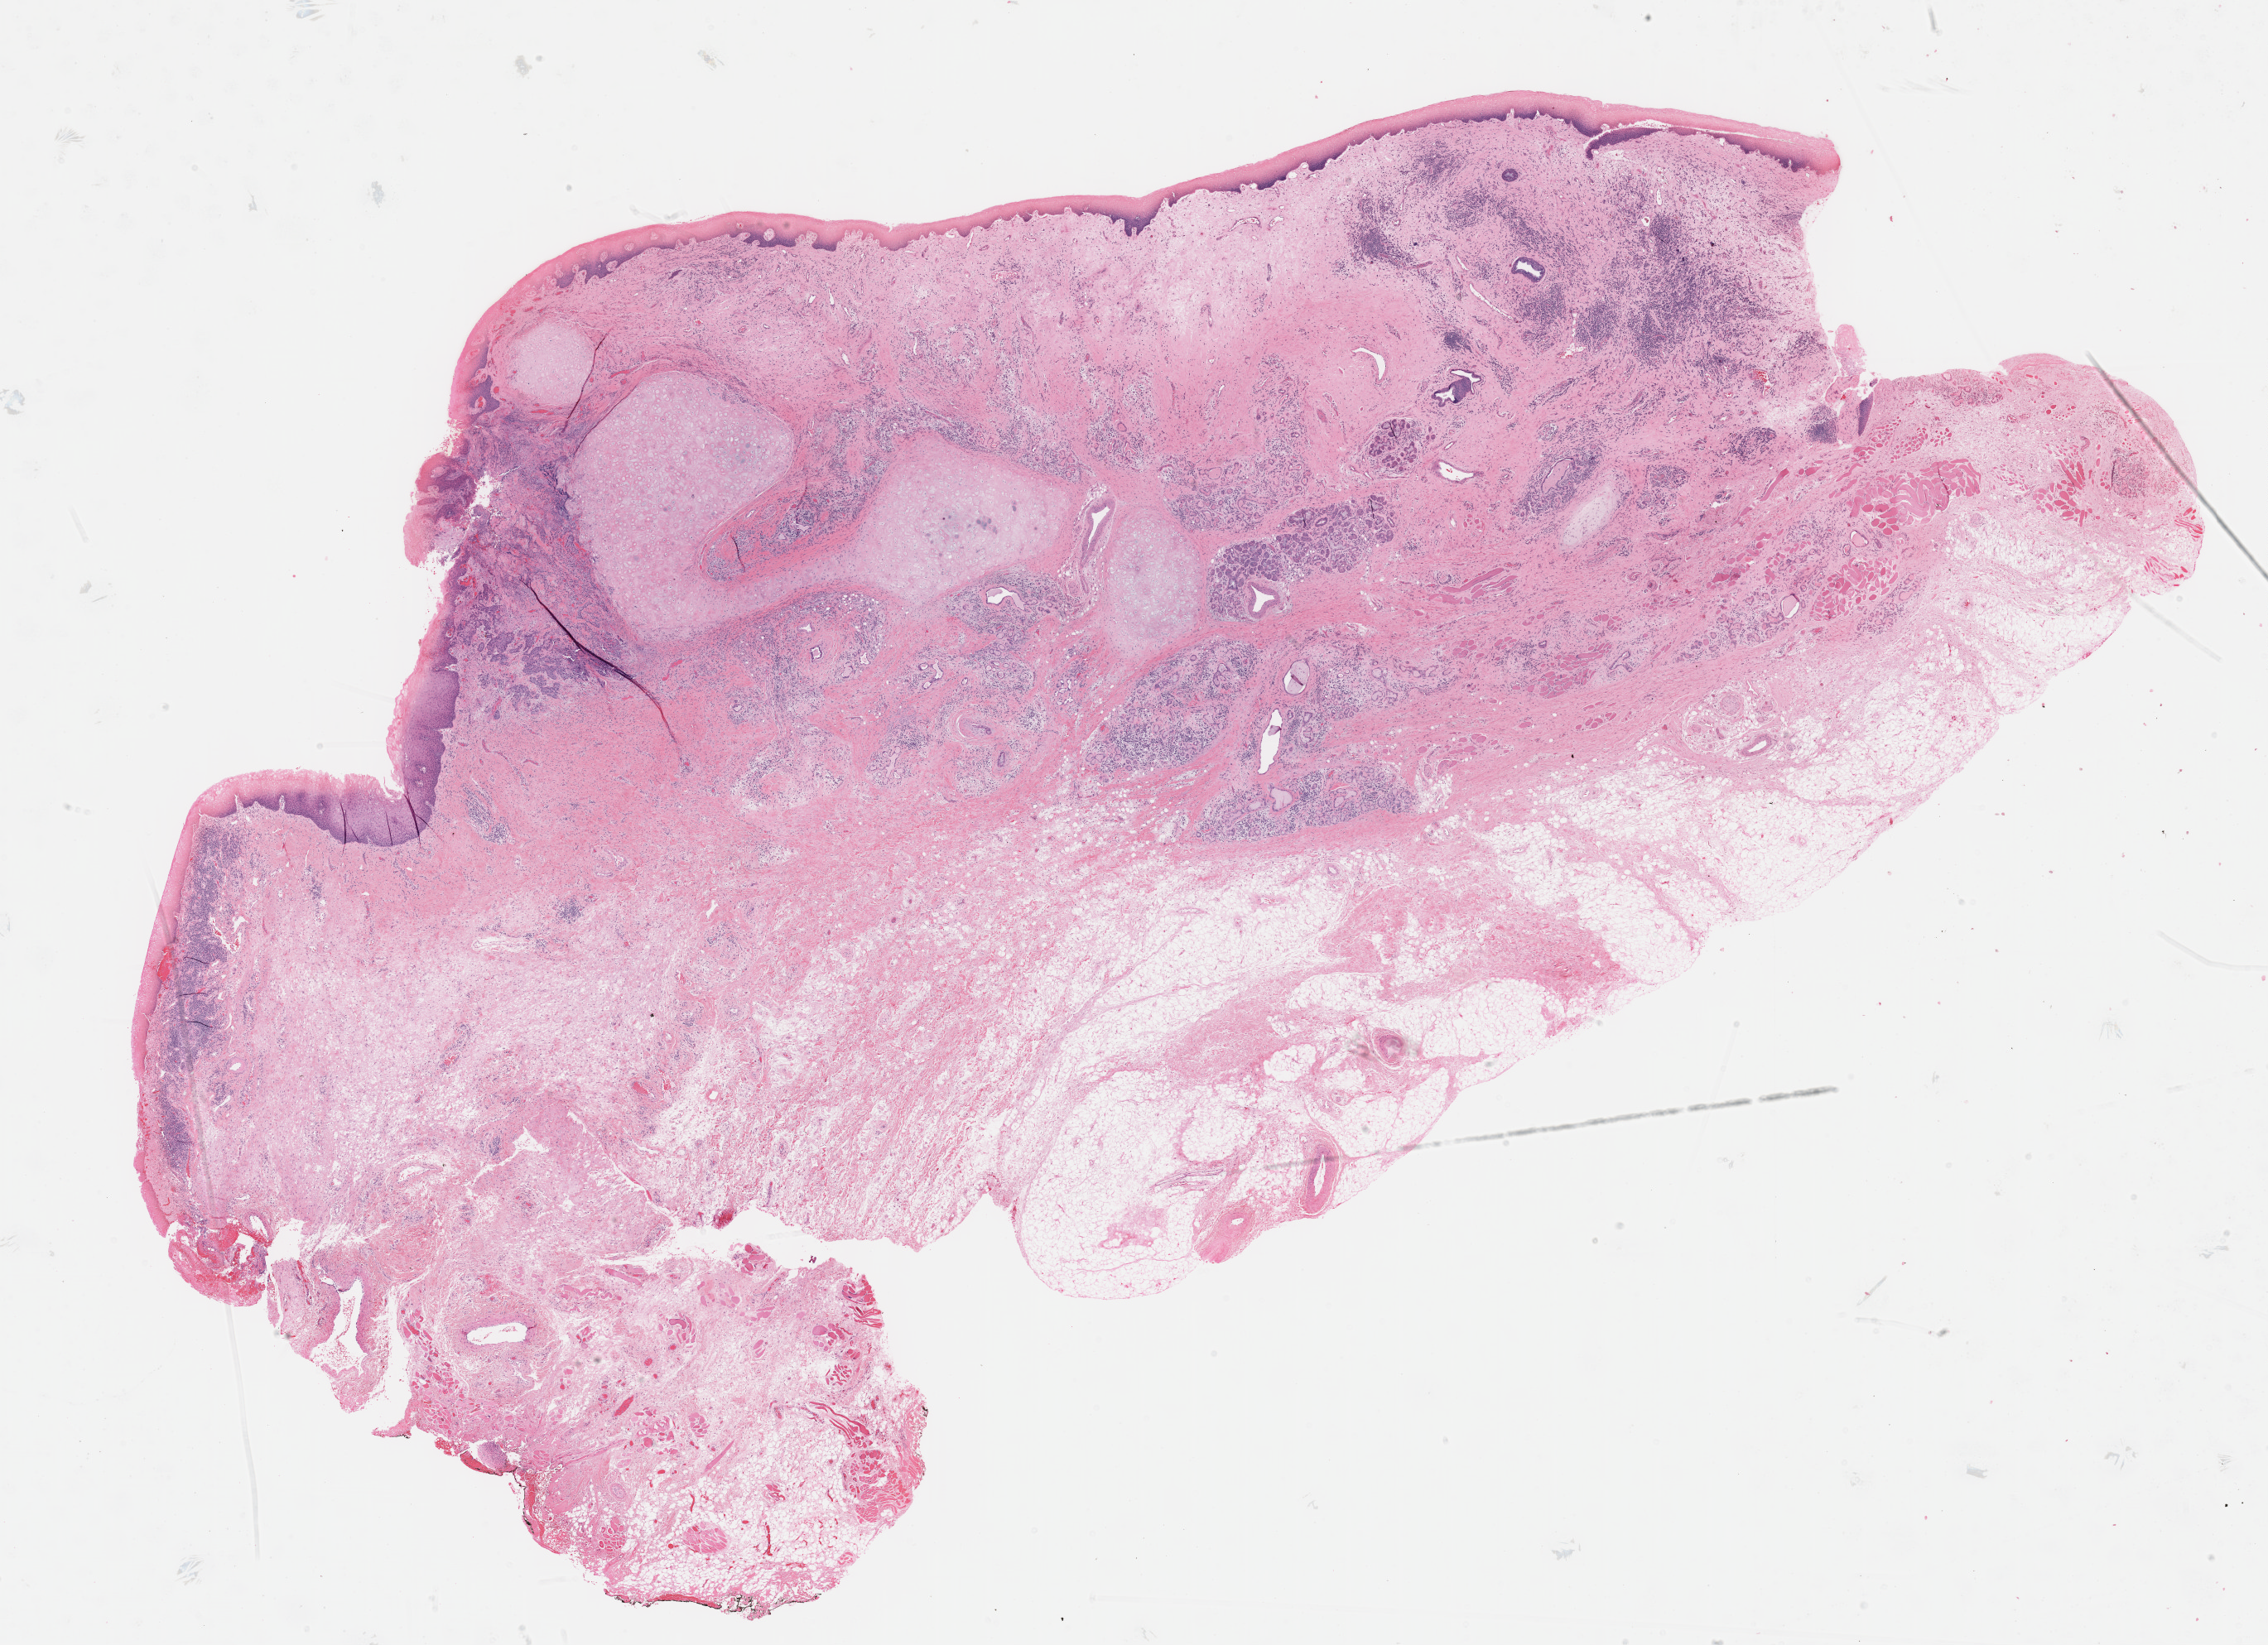
Digitized Hematoxylin and eosin (H&E) stained tissue section (whole slide) — a low-resolution overview of the entire scanned area, about 22.1 x 16.1 mm (acquisition: 40x scan); formalin-fixed paraffin-embedded (FFPE) diagnostic section; primary tumour sample from the head and neck. Patient: male, age at initial diagnosis 38 years. Histologic grade: GX (grade cannot be assessed).
TNM: T2 NX. Diagnosis: Squamous cell carcinoma, NOS (larynx, NOS). AJCC pathologic stage: II (7th edition).